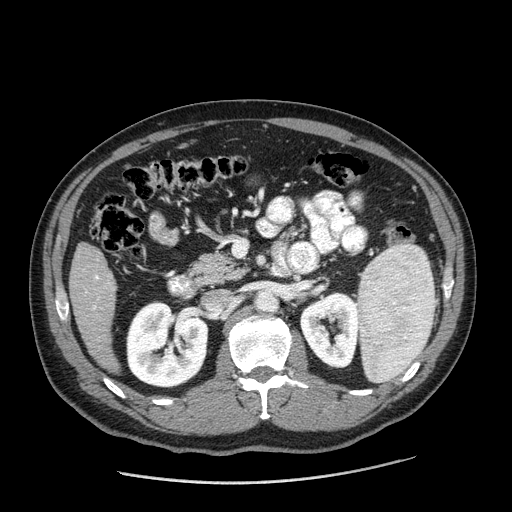
Contrast-enhanced abdominal CT (liver protocol), one axial slice; slice 67 of 198 in the series (ordered by position); one of 2 acquisitions stored at this slice position; soft-tissue window (W 400 / L 40 HU); 2.5 mm slice thickness; 512 × 512 image matrix, field of view 400 × 400 mm. Case-level facts recorded for this patient, not image findings: diagnosis: hepatocellular carcinoma (patient treated with transarterial chemoembolisation; whether this scan precedes or follows treatment is not stated here); TNM stage (as recorded): Stage-II; Child-Pugh class: A; tumour differentiation: moderately differentiated.
Annotated regions visible in this slice (semi-automatically segmented with operator editing):
- liver parenchyma outside the tumour (the mass and vessels are separate outlines, so this box may not span the whole liver): bounding box <68,242,120,372> (left, top, right, bottom; pixels)
- liver vessels: <94,275,99,308>